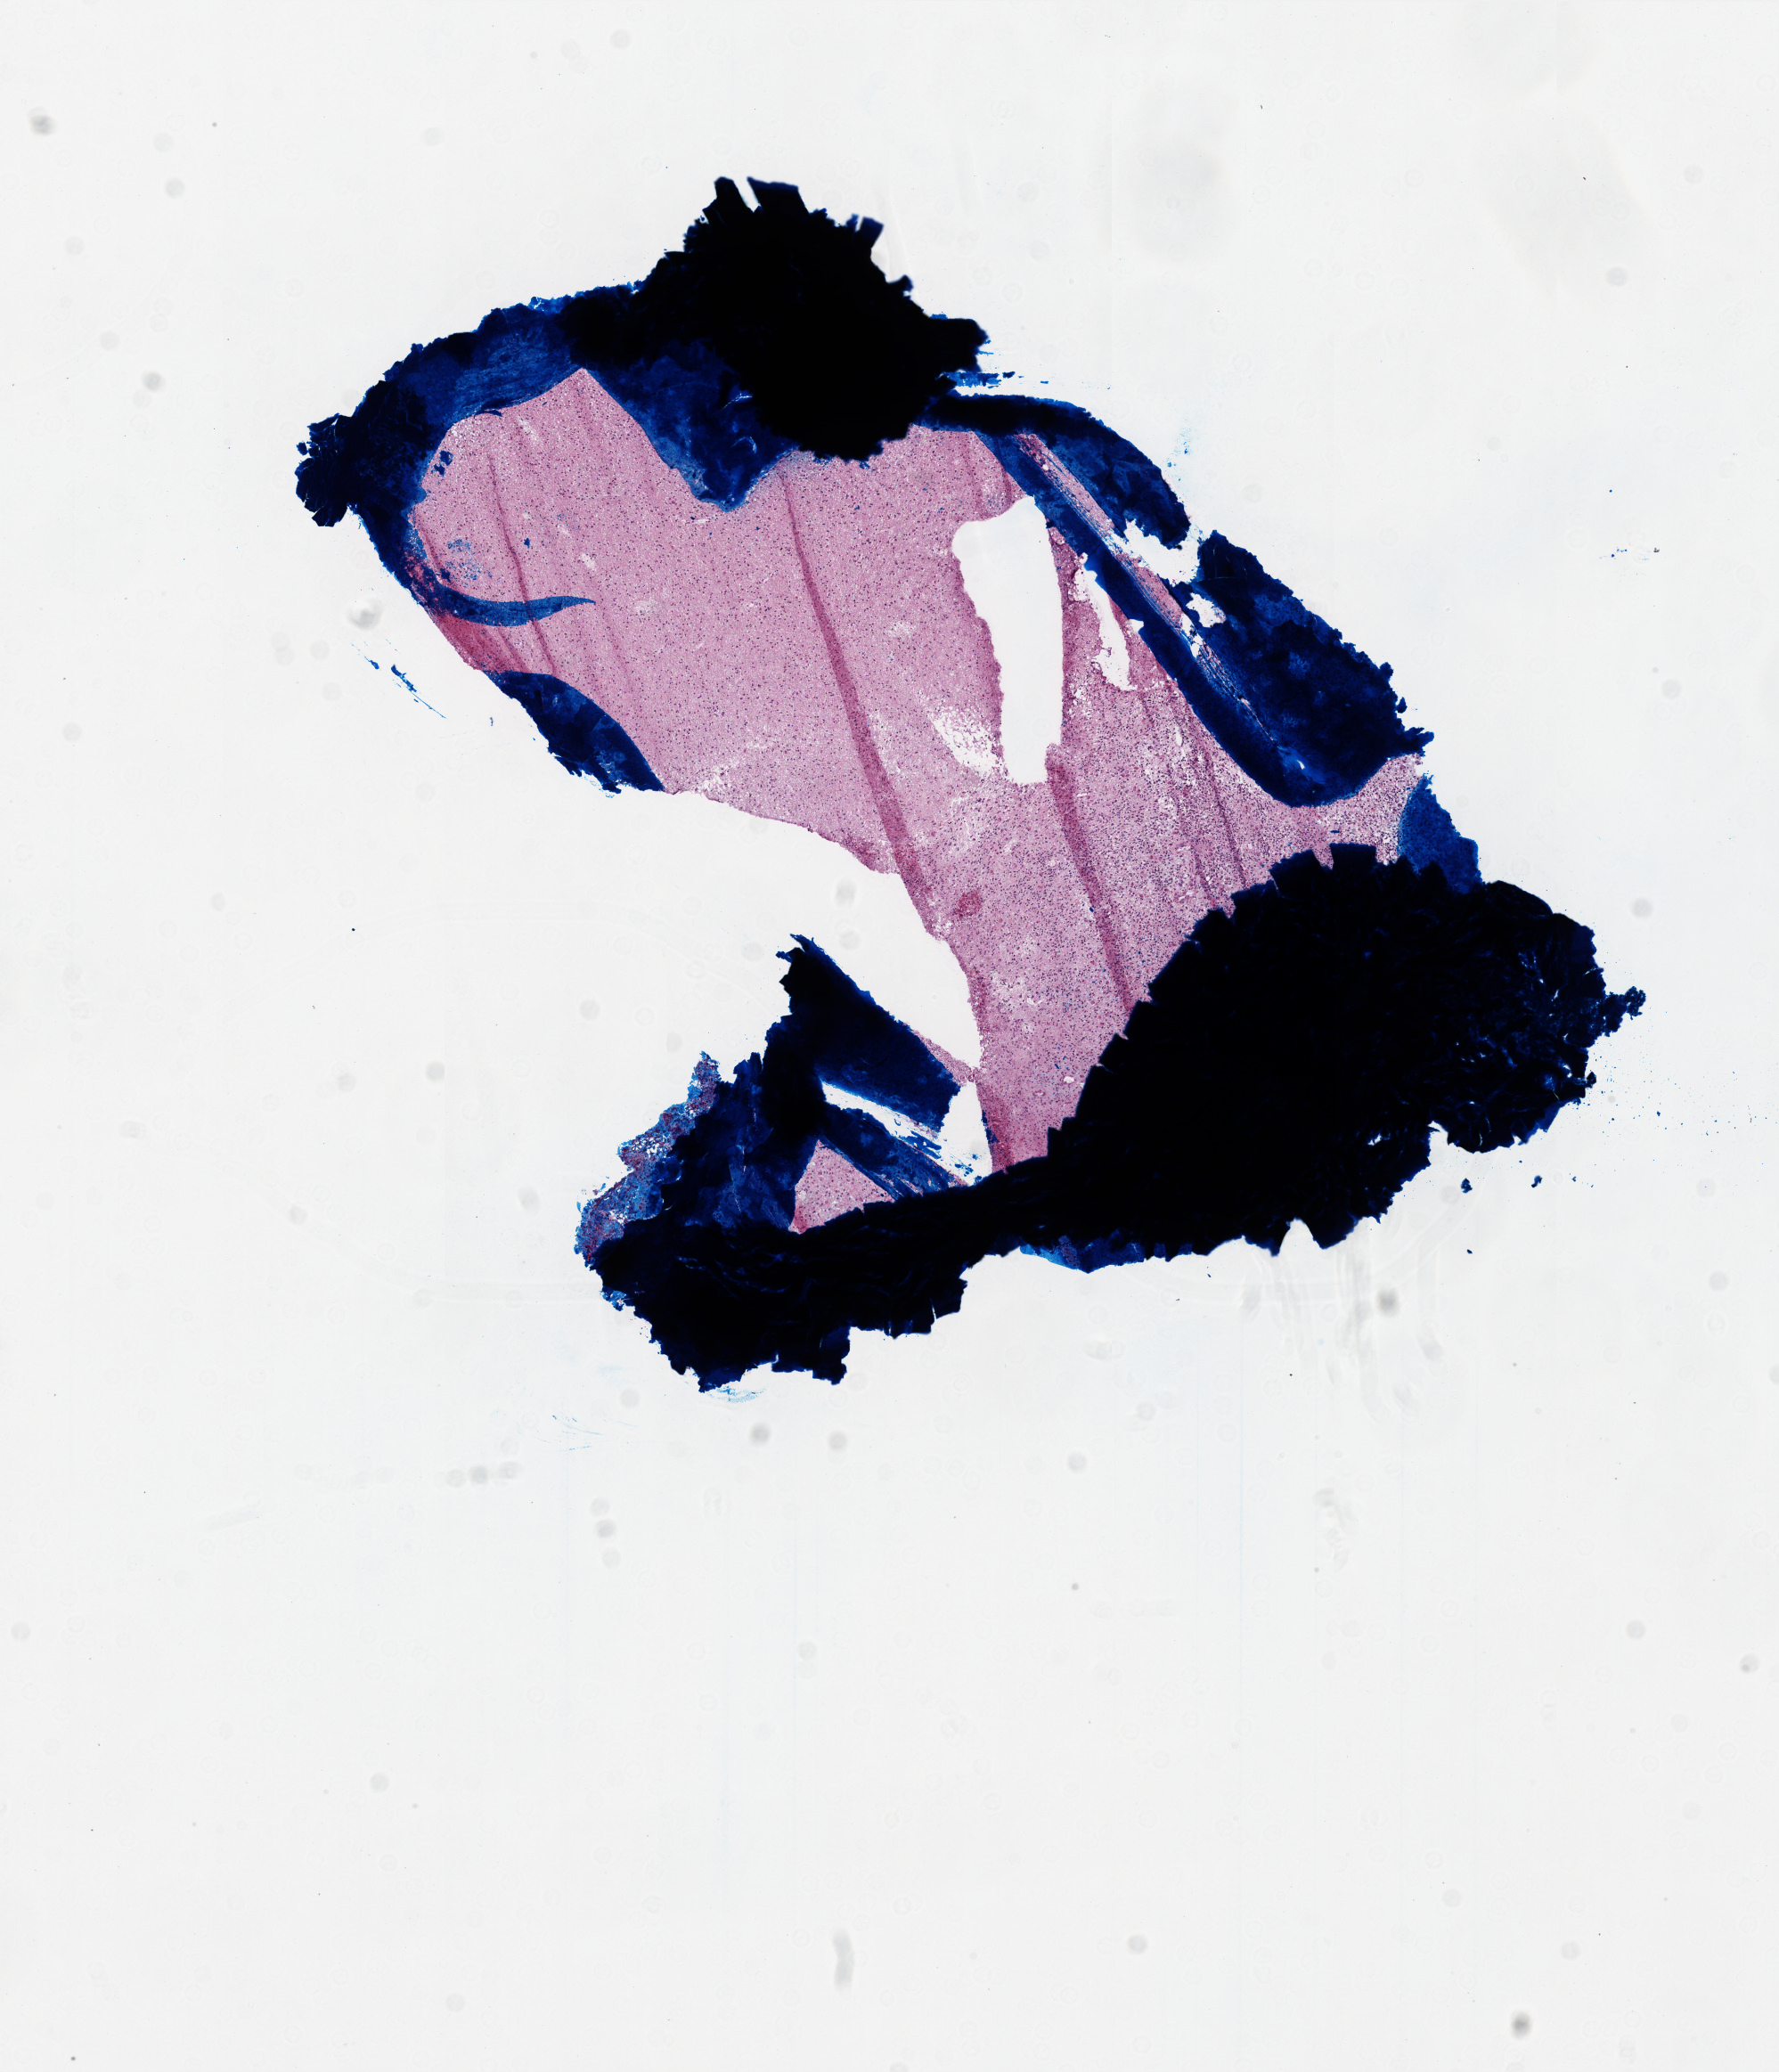
Digitized Hematoxylin and eosin (H&E) stained tissue section (whole slide) — low-resolution overview of the scanned area, about 8.0 x 9.3 mm (acquisition: 20x scan), frozen section from the top of the tissue portion, primary tumour sample from the brain. Patient: male, age at initial diagnosis 65 years. Slide review estimates, as recorded: tumour cells 50%, tumour nuclei 90%, normal cells 0%, stromal cells 50%, necrosis 0%.
Pathologic diagnosis: Glioblastoma.